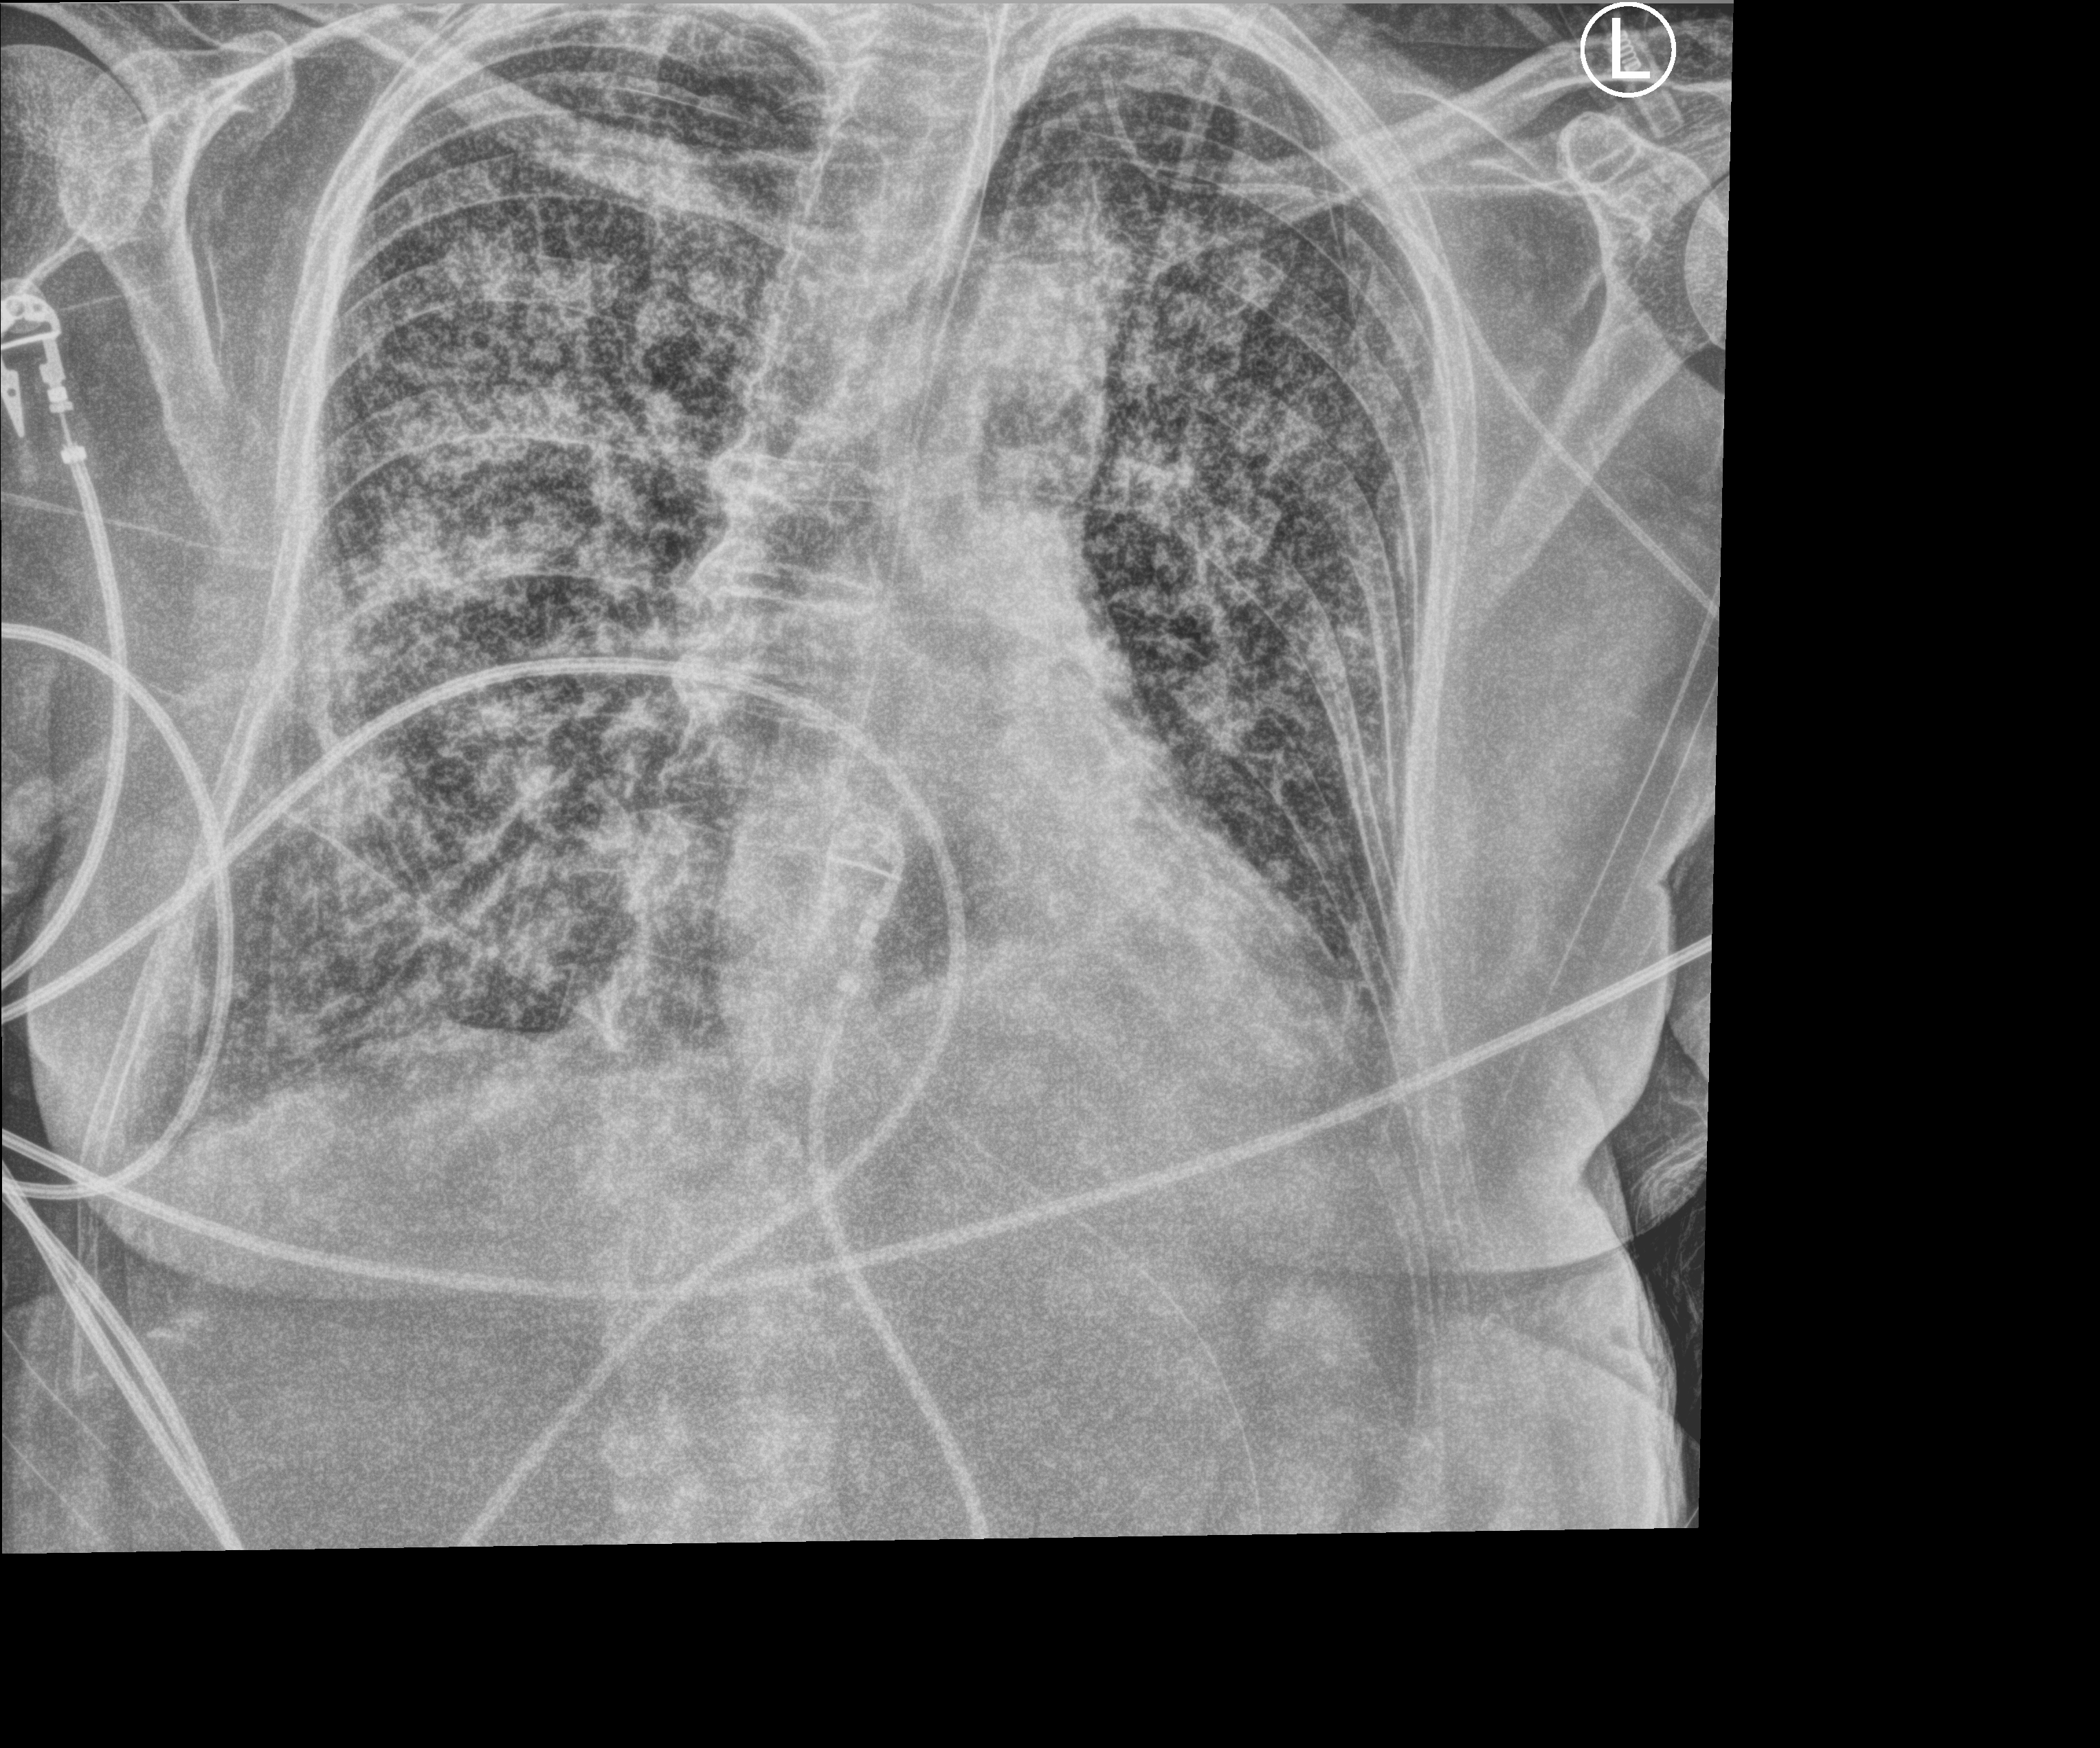
Chest X-ray (portable). Patient hospitalised with COVID-19; female, aged 75–90 years.
Hospital-stay facts (about this admission, not read from this image; timing relative to this image not recorded): length of hospital stay: 70 days; admitted to intensive care during this hospital stay: yes.